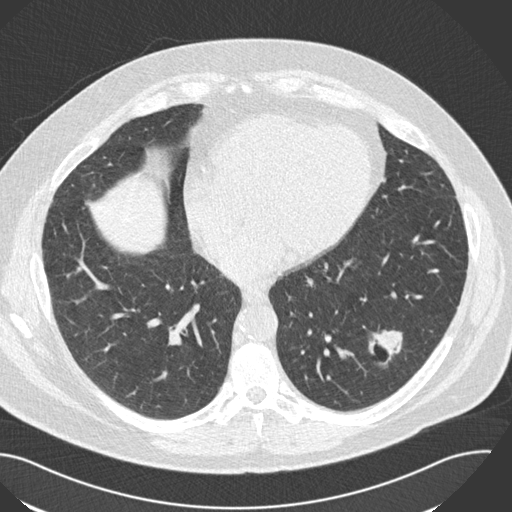
Low-dose screening chest CT, one axial slice; 120 kVp; lung window (W 1500 / L -600 HU); 2 mm slice thickness; 512 × 512 image matrix, field of view 394 × 394 mm.
Outlined on this slice (outlined manually by an expert reader):
- lesion 1 (tumor, lower lobe of left lung): bounding box (x1, y1, x2, y2) in pixels: (373, 330, 402, 364)